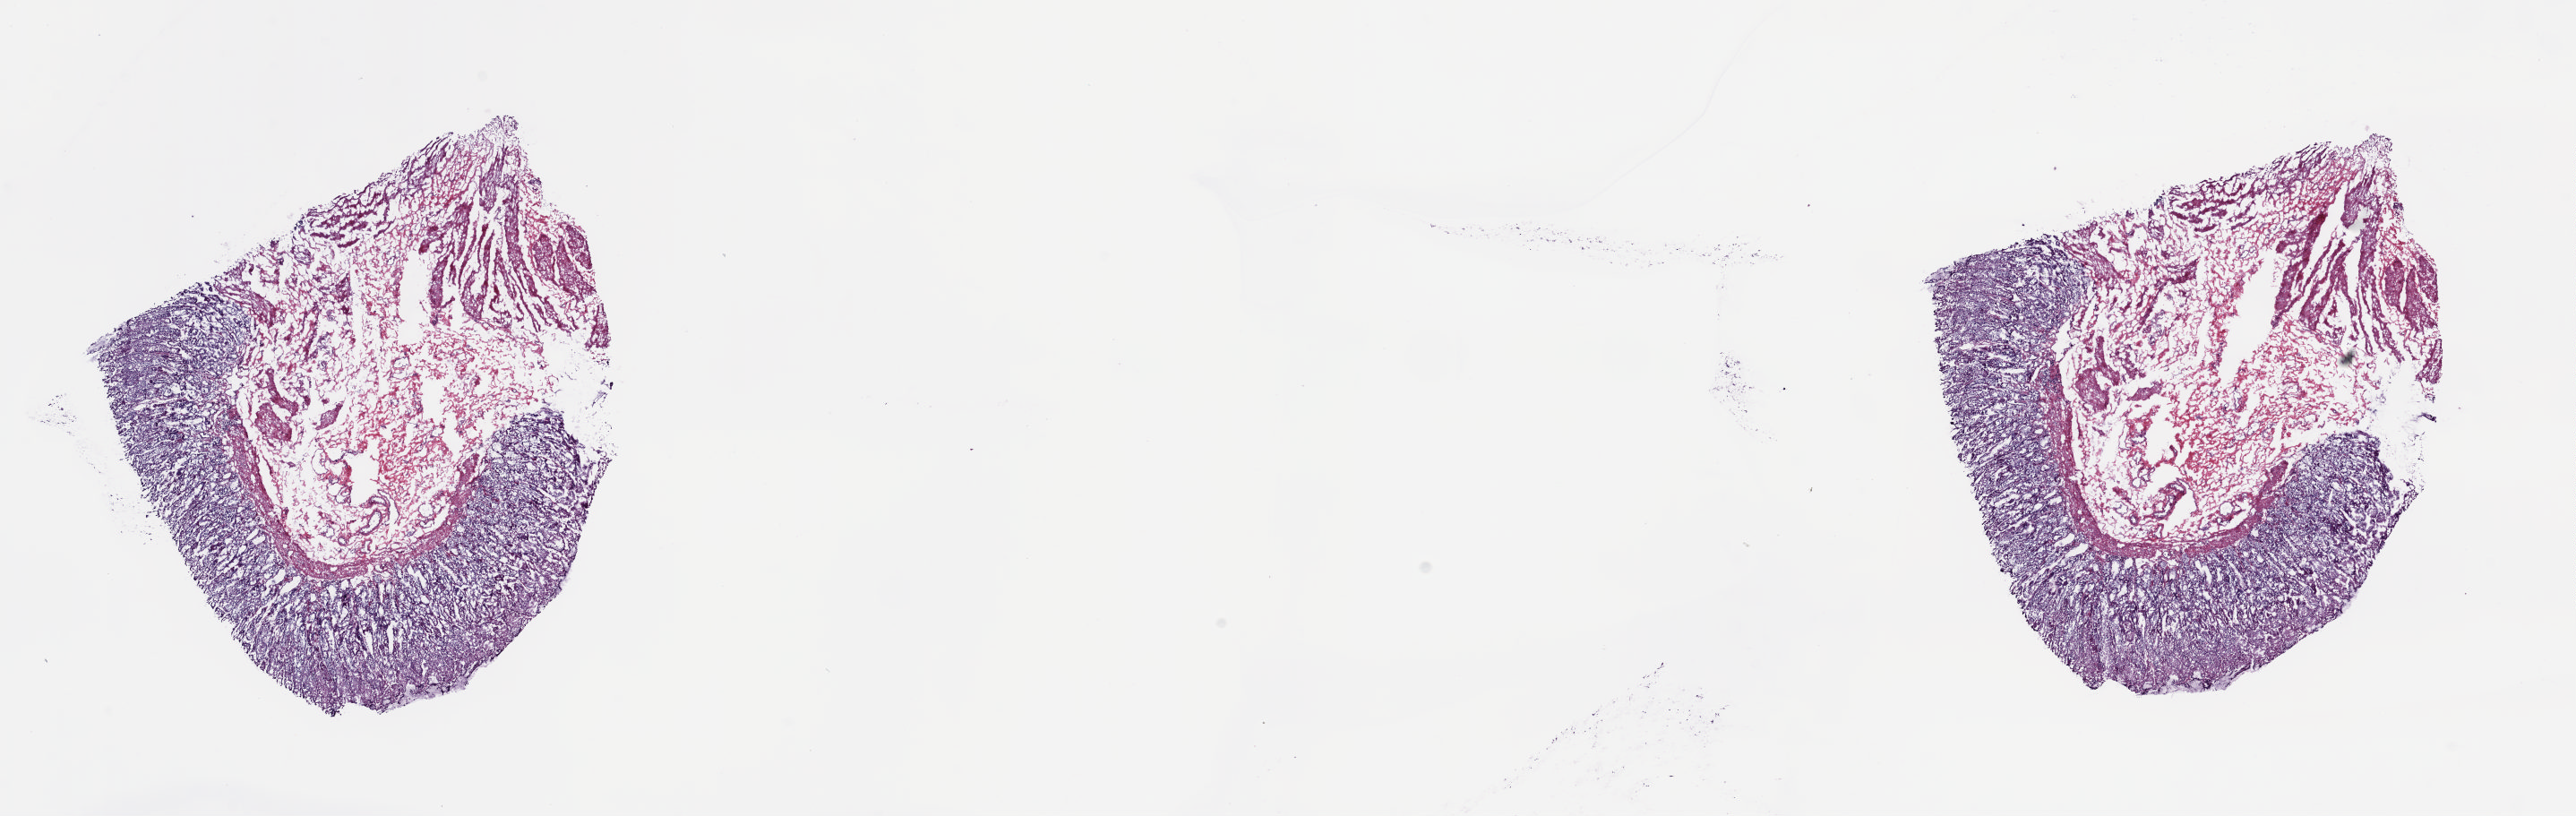
Digitized Hematoxylin and eosin (H&E) stained tissue section (whole slide) — shown as a low-resolution overview of the whole scanned area (about 22.8 x 7.2 mm). Frozen section from the top of the tissue portion. Esophagus, solid tissue normal (non-tumour tissue) sample. Male patient; age at initial diagnosis 58 years. Slide review estimates, as recorded: tumour cells 0%, tumour nuclei 0%, normal cells 25%, stromal cells 75%, necrosis 0%. Infiltration values recorded for this section: lymphocyte infiltration 8%, monocyte infiltration 0%, neutrophil infiltration 0%.
* this section: solid tissue normal sample (biorepository sample class)
* patient diagnosis: Adenocarcinoma, NOS (lower third of esophagus)